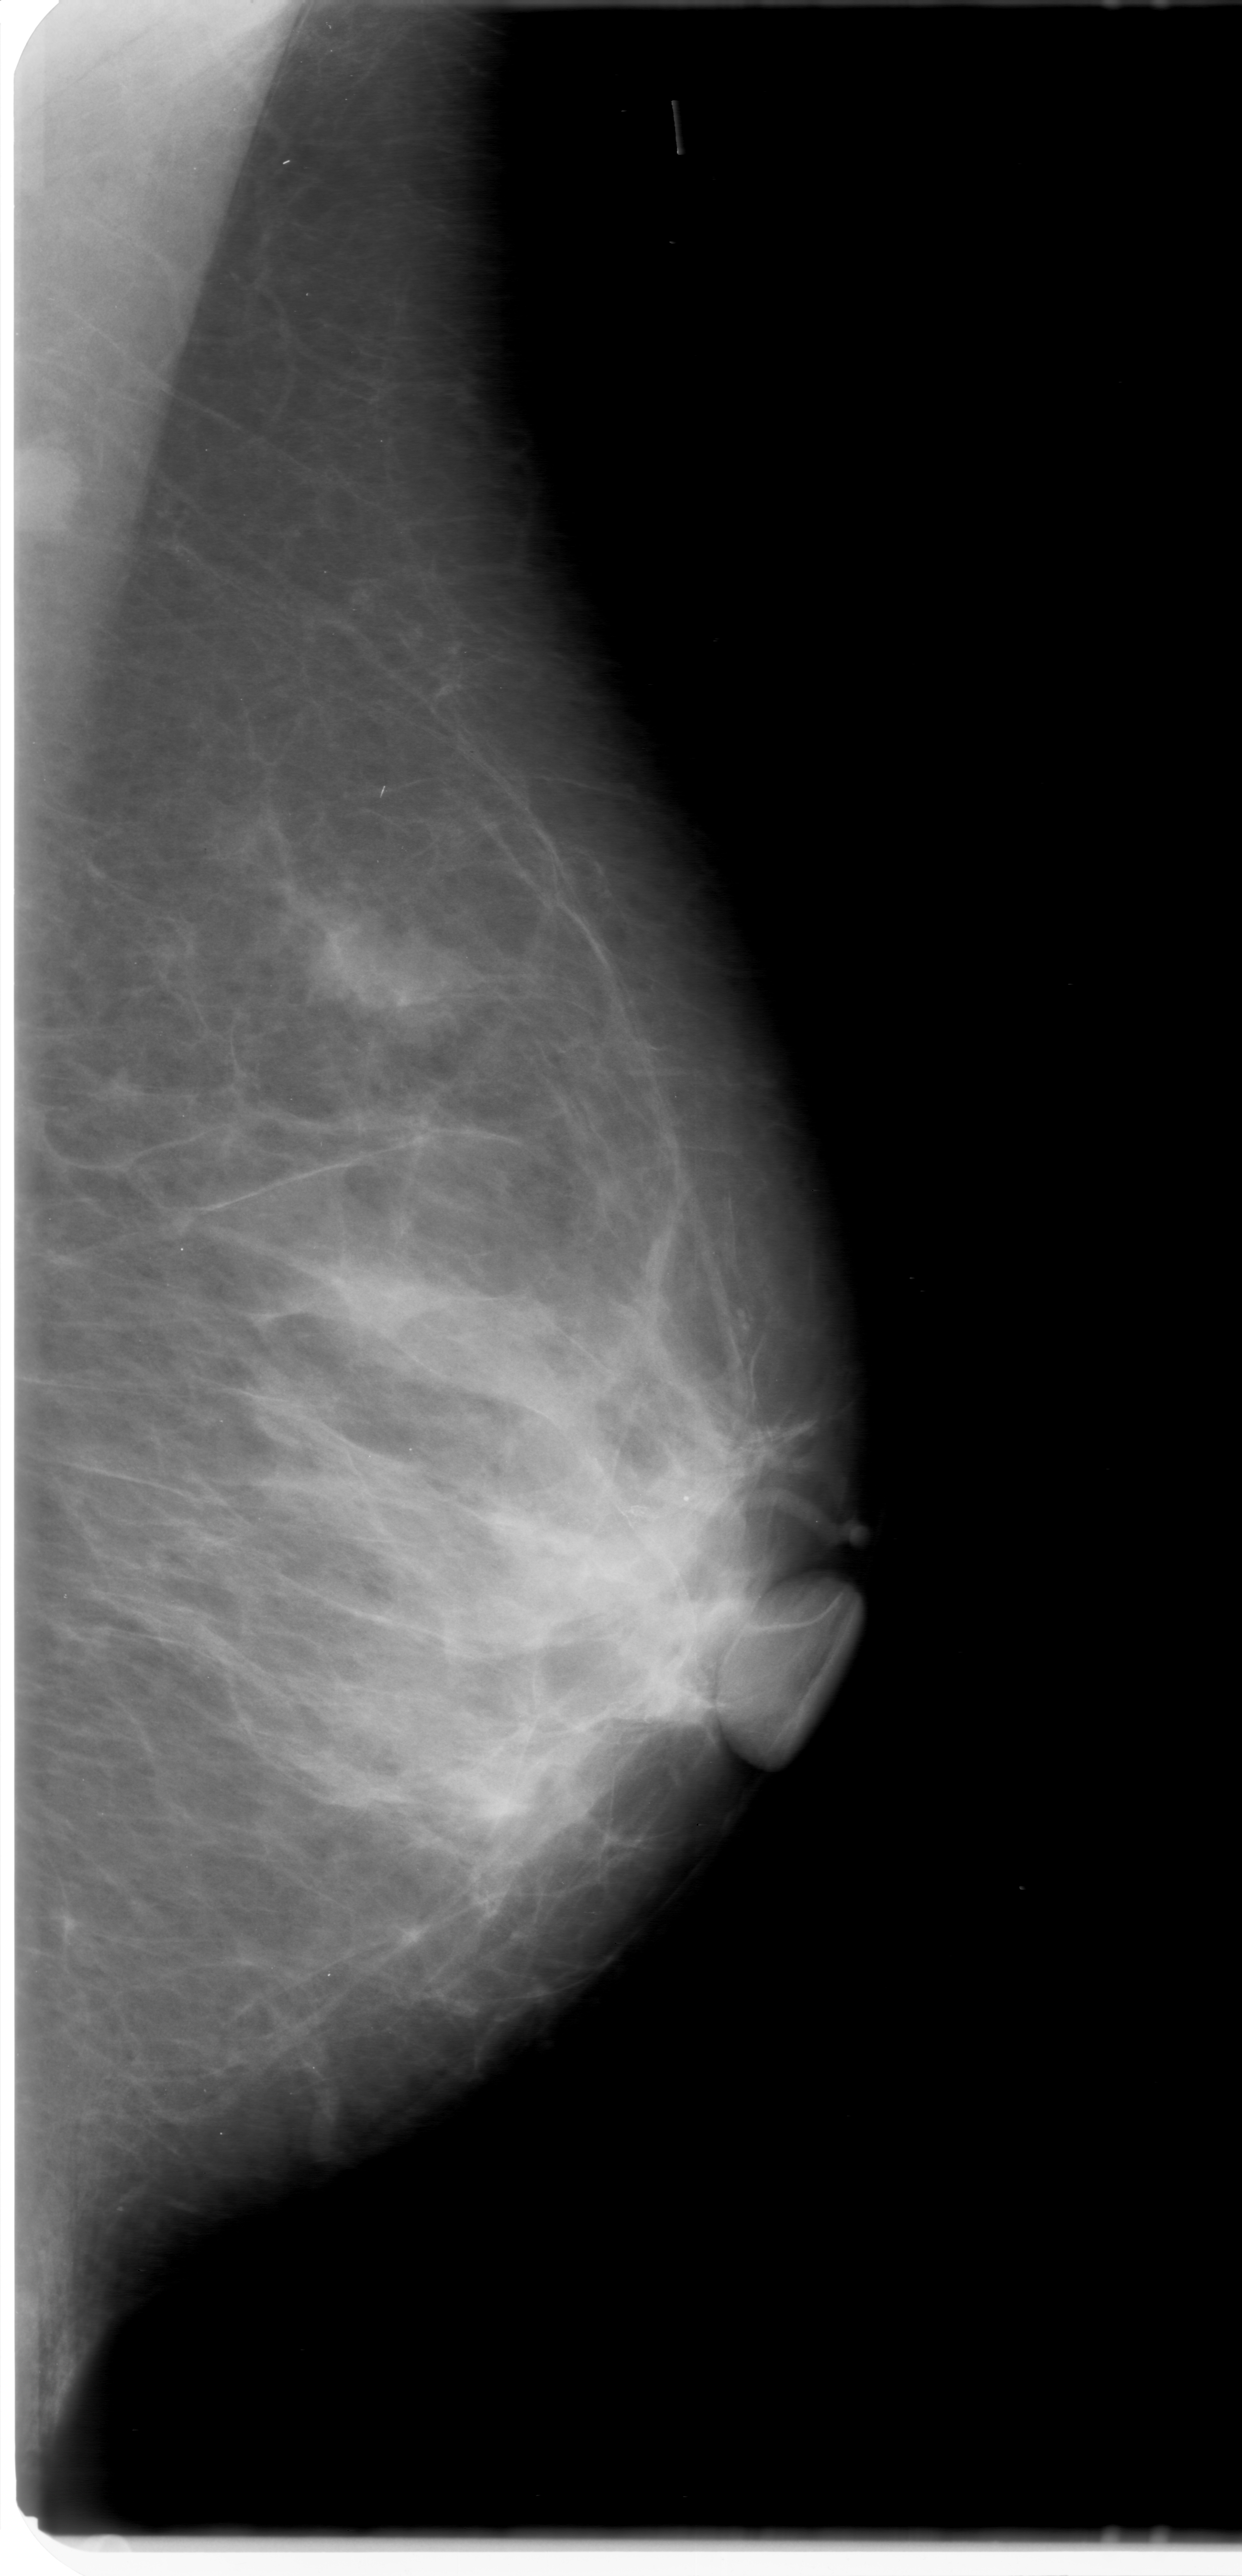
Digitized screen-film mammogram, left breast, mediolateral oblique (MLO) view, BI-RADS breast density category 2 (scale 1–4).
- Mass, shape lobulated, margins obscured; BI-RADS assessment category 0 (incomplete: needs additional imaging); pathology result (as recorded, not read from the image): malignant.